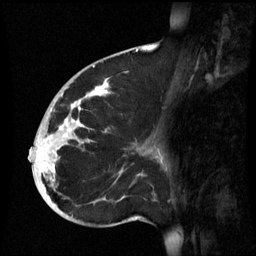
Breast MRI (dynamic contrast-enhanced), one sagittal slice; slice 27 of 60 in the series (ordered by position); dynamic contrast-enhanced series, image 2 of 3 at this slice position (ordered by acquisition); 1.5 T; TE 4.2 ms, TR 8.9 ms; 2.6 mm slice thickness; 256 × 256 image matrix. Patient: female, 35 years. From the clinical record (not read from this slice): setting: breast cancer imaged before/during neoadjuvant chemotherapy; receptor status: HR-positive, HER2-negative.
Structures marked on this image (semi-automatic segmentation, software-assisted and operator-edited):
- analysis volume of interest (the breast-tissue region the enhancement analysis was run in; not a lesion): bounding box (x1, y1, x2, y2) in pixels: (32, 74, 164, 221)
- tumour enhancement mask (voxels above the 70 % enhancement threshold inside the analysis volume of interest): (37, 80, 109, 179)